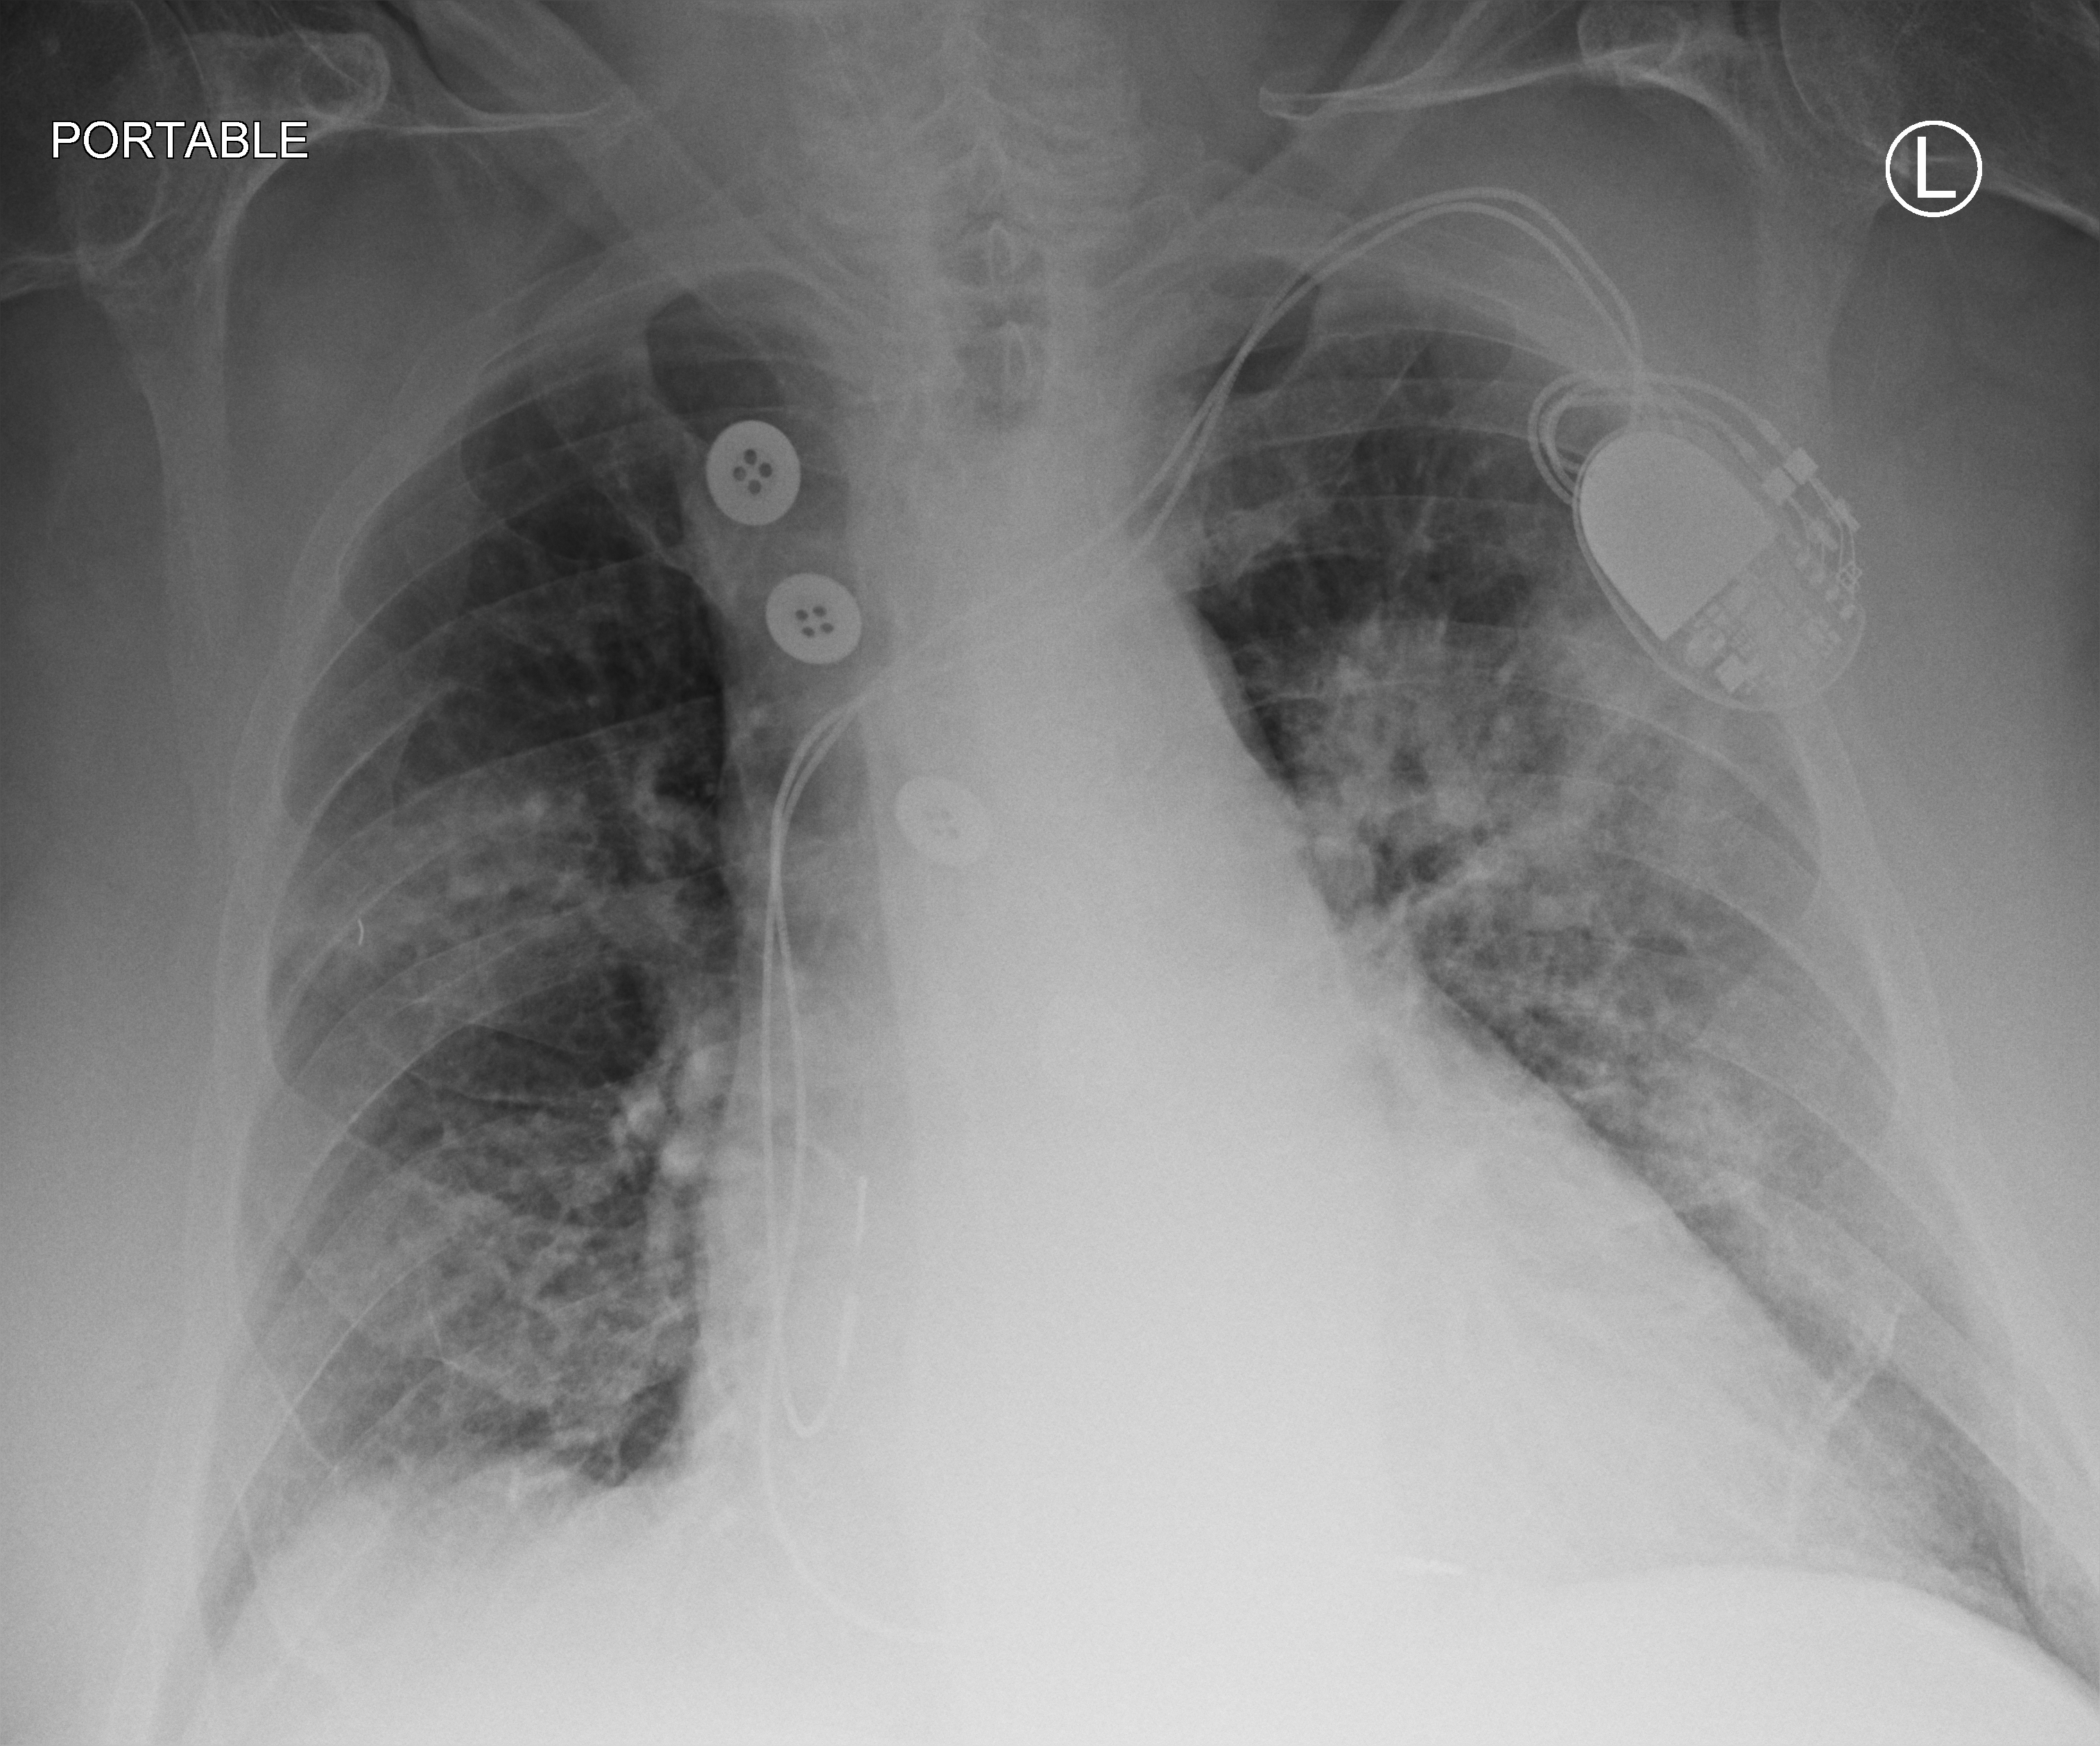
Bedside chest radiograph (computed radiography), anteroposterior (AP) projection. Male patient hospitalised with COVID-19, age 75–90 years.
From the hospital-stay record, not from the radiograph (when in the stay this image was taken is not recorded): mechanically ventilated during this hospital stay: no.